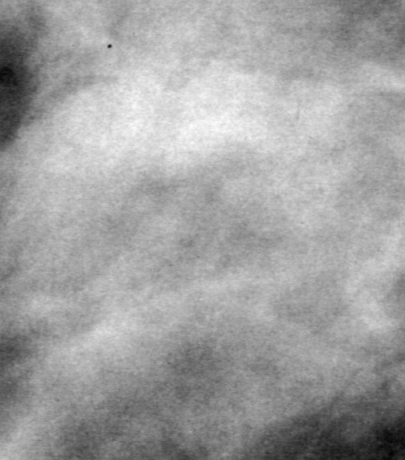
Cropped region of a digitized screen-film mammogram centred on a radiologist-marked abnormality, left breast, MLO view, BI-RADS breast density category 4 (scale 1–4).
Marked abnormality: mass, shape oval, margins obscured; BI-RADS assessment category 3; subtlety rating 2 on a 1 (subtle) to 5 (obvious) scale; pathology (as recorded): benign.